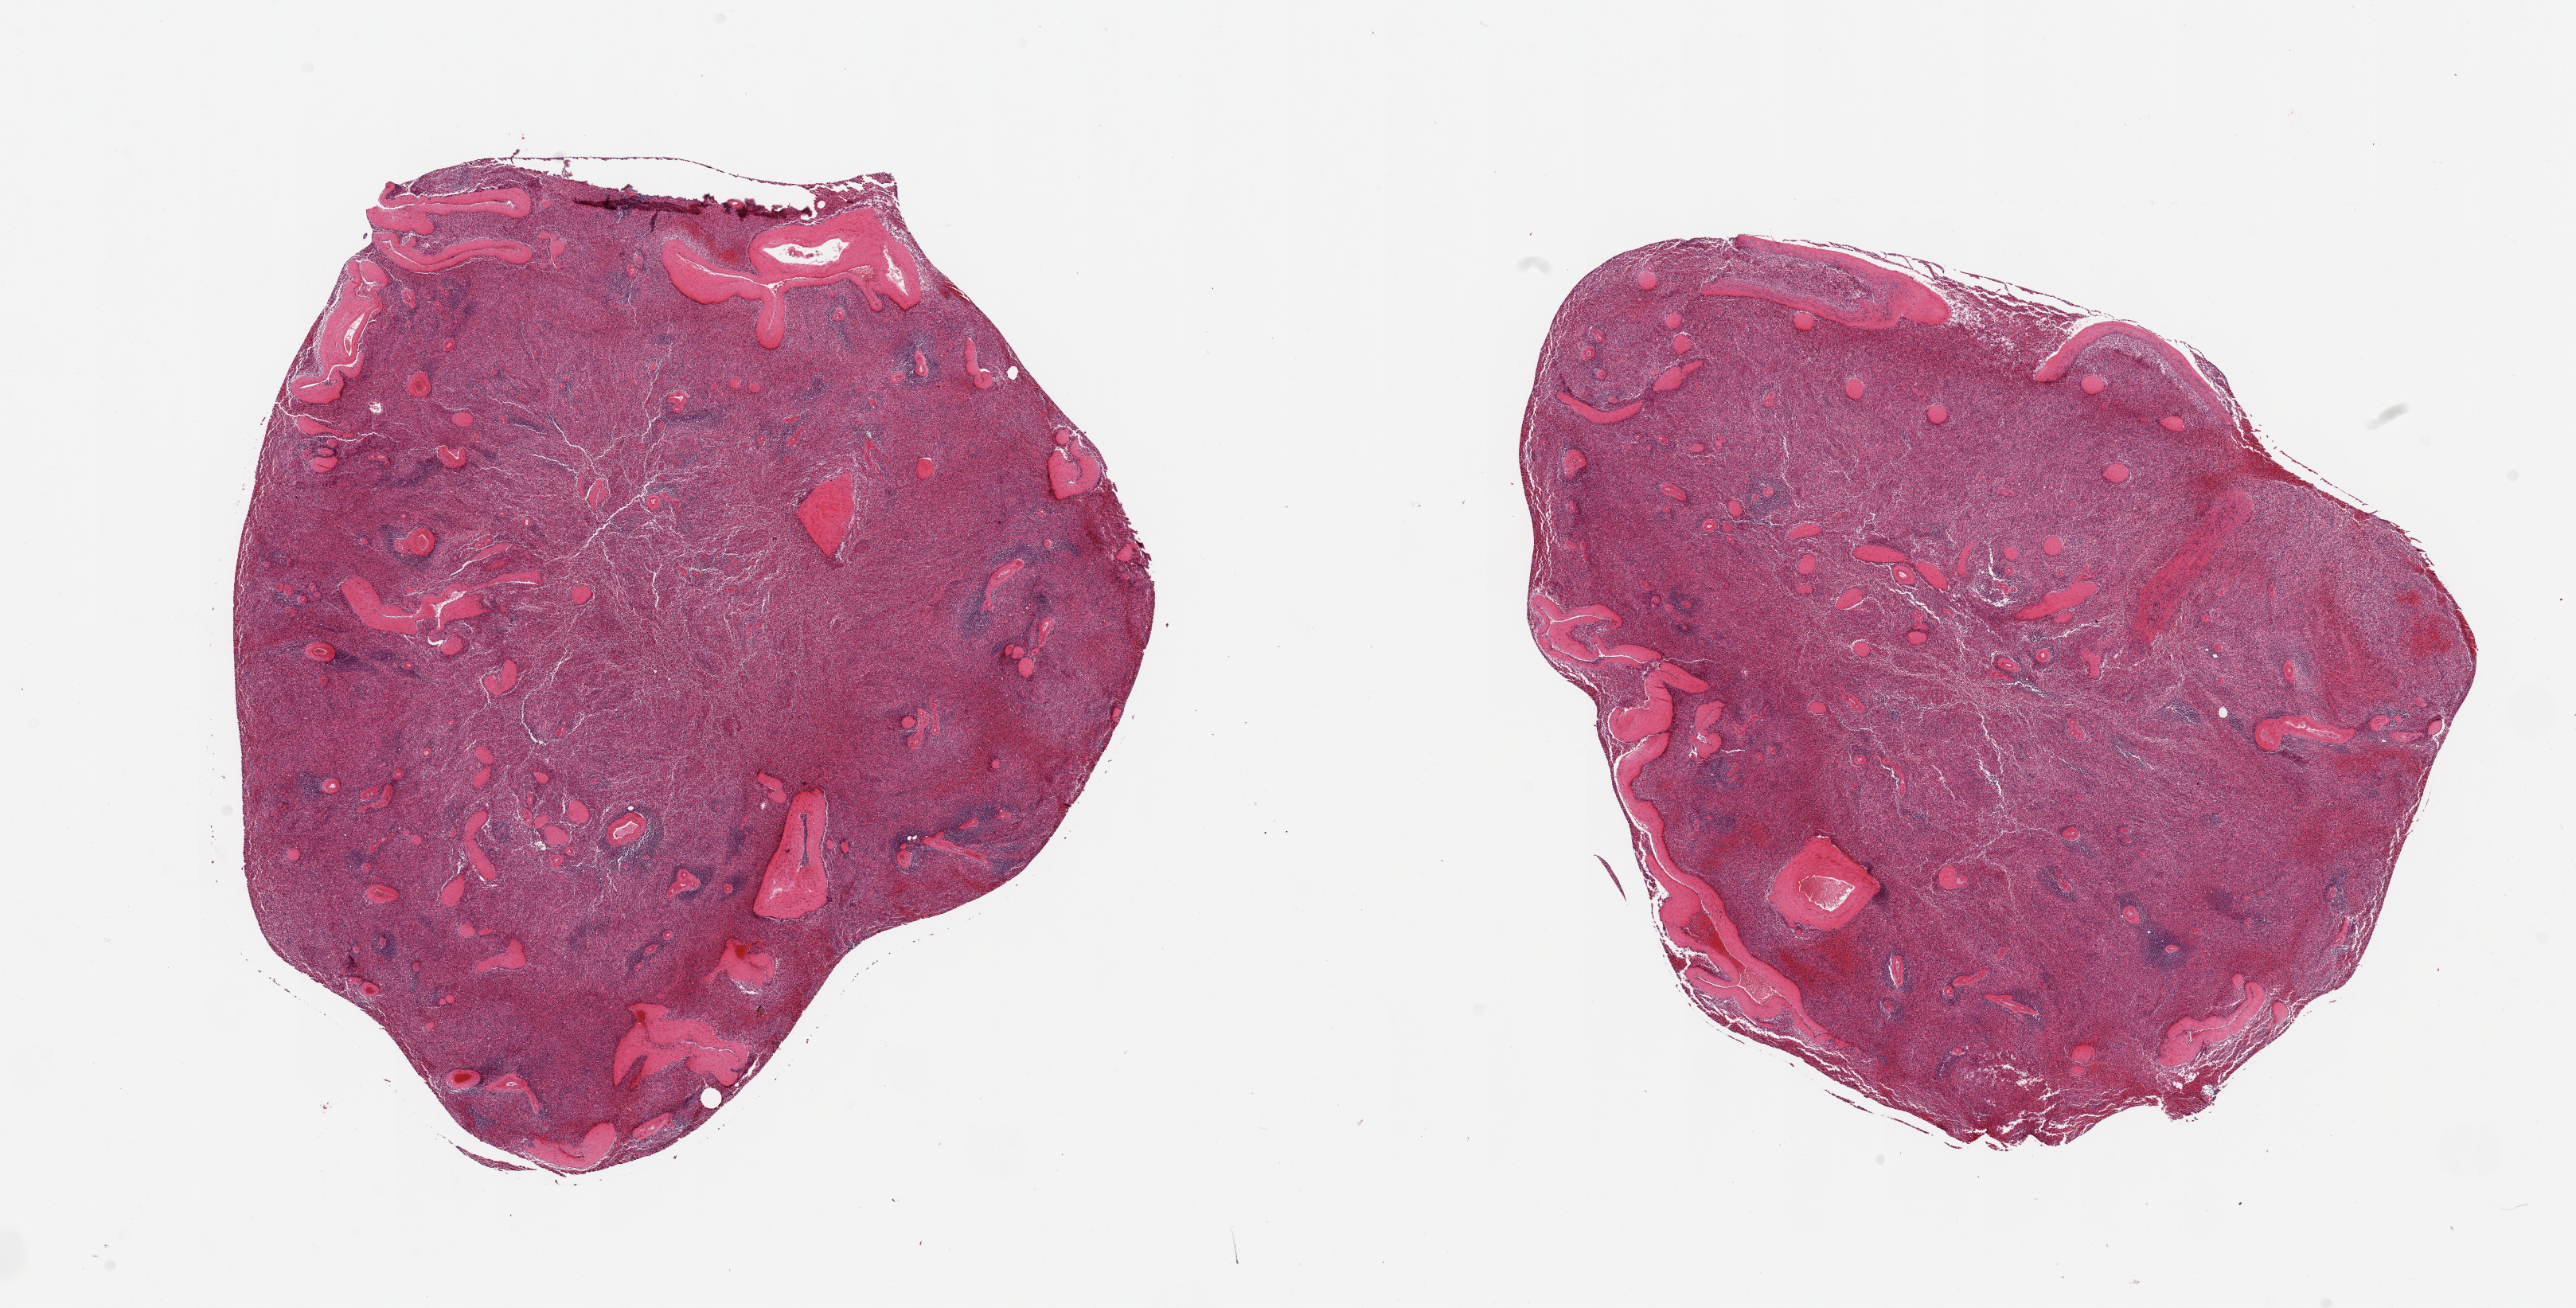
Whole-slide image, haematoxylin and eosin stain, whole scanned area (about 25.6 x 13.0 mm, acquisition: 20x scan) shown as a low-resolution overview. PAXgene-fixed paraffin-embedded (PFPE) section. Sampled site (target tissue): spleen. Donor tissue sample. Donor sex: male.
Reviewer comment on this tissue sample: 2 pieces.